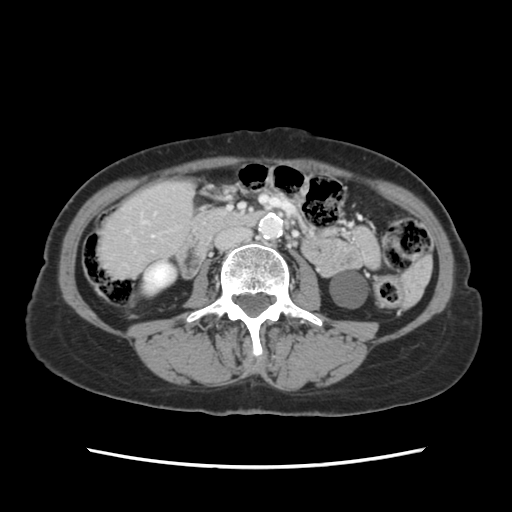
Contrast-enhanced abdominal CT, one axial slice; 120 kVp; soft-tissue window (W 400 / L 40 HU); 512 × 512 image matrix, field of view 330 × 330 mm. Female patient, age 70 years. Case-level facts recorded for this patient, not image findings: diagnosis: colorectal cancer liver metastases, imaged before liver resection; multiple liver metastases: no; largest metastasis: 2.5 cm; disease in both lobes: no.
Annotated regions visible in this slice (outlined manually by an expert reader):
- liver: bounding box (x1, y1, x2, y2) in pixels: (101, 182, 190, 276)
- planned liver remnant (the part of the liver to remain after resection): (101, 182, 190, 275)